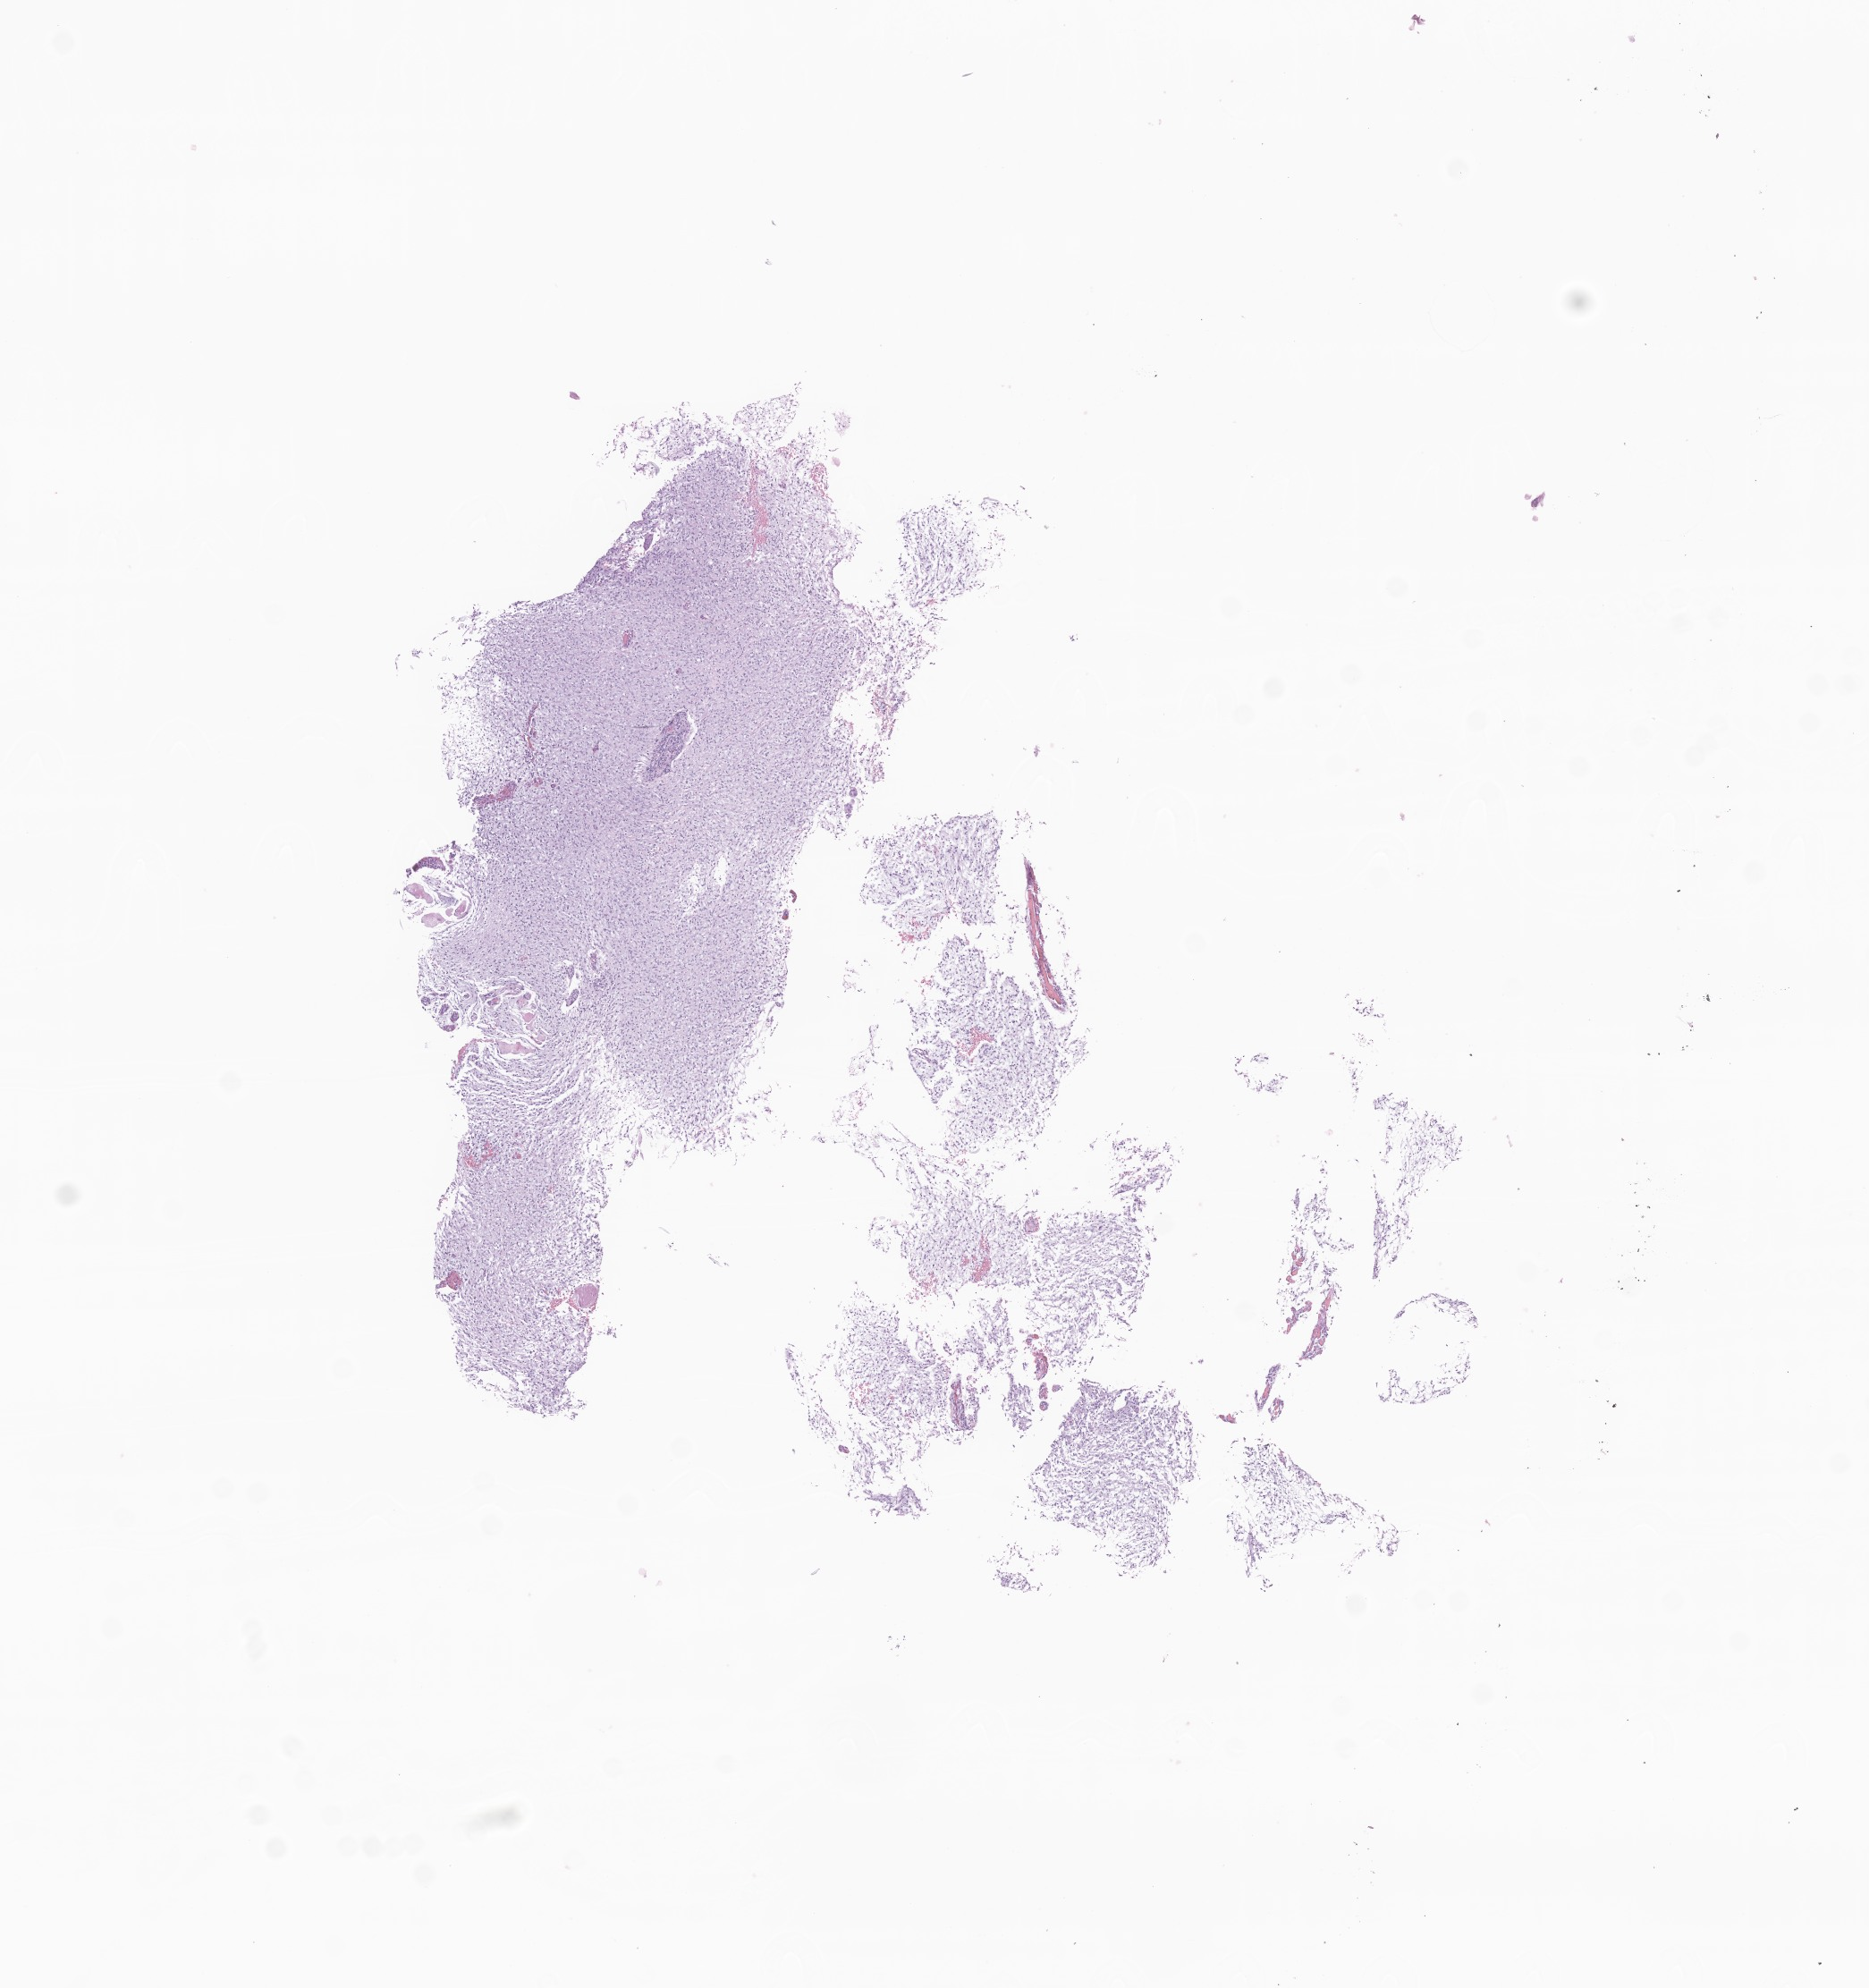
Digitized H&E-stained section of tumor tissue from the spinal cord, low-resolution overview of the scanned area, about 8.8 x 9.4 mm; FFPE section. Male patient, age 659 days (about 1.8 years).
Diagnosis (ICD-O-3 morphology term): Neoplasm, malignant.